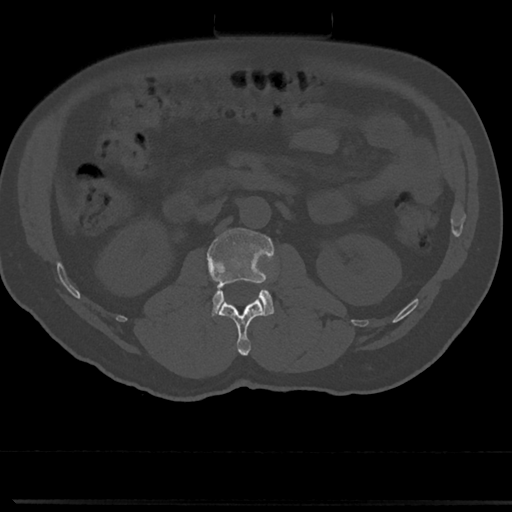
CT including the spine, one axial slice. Slice 43 of 817 in the series (ordered by position). Reconstruction kernel Br40s/3. 120 kVp. Bone window (W 1800 / L 400 HU). 512 × 512 image matrix, field of view 355 × 355 mm. Male patient, age 61 years. Case-level facts recorded for this patient, not image findings: primary cancer: prostate.
Annotated regions visible in this slice (semi-automatically segmented with operator editing):
- L1 vertebra: box from (x=219, y=299) to (x=264, y=355) px
- L2 vertebra: (x=208, y=227)–(x=273, y=316)